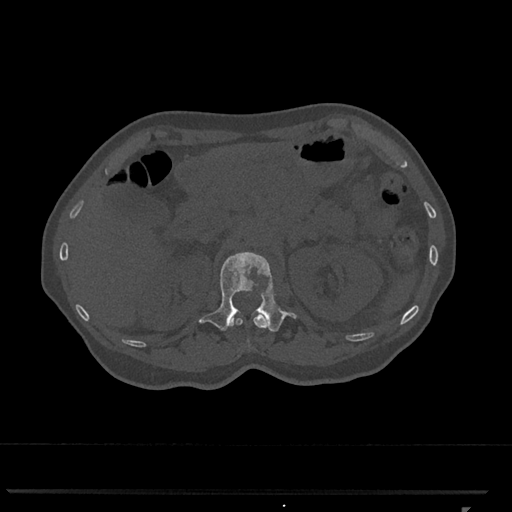
CT including the spine, one axial slice; position 418 of 793 along the scan axis; 120 kVp; bone window (W 1800 / L 400 HU); 0.5 mm slice thickness; 512 × 512 image matrix, field of view 380 × 380 mm. Female patient, age 62 years. Case-level facts recorded for this patient, not image findings: primary cancer: renal.
Annotated regions visible in this slice (semi-automatically segmented with operator editing):
- L1 vertebra: bounding box [x1, y1, x2, y2] px = [198, 252, 297, 332]
- T12 vertebra: [230, 313, 267, 328]